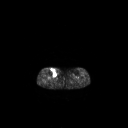
FDG PET of an extremity soft-tissue mass (from a PET/CT study), one axial slice; position 142 of 267 along the scan axis; 3.27 mm slice thickness; 128 × 128 image matrix, field of view 700 × 700 mm. Patient: female, 65 years. Case-level facts recorded for this patient, not image findings: histological type: undifferentiated – high grade; grade: high; site of the primary tumour: right thigh.
Outlined on this slice (expert contour drawn on MRI and transferred to this co-registered scan by the dataset authors):
- gross tumour volume (mass): box from (x=50, y=68) to (x=57, y=75) px